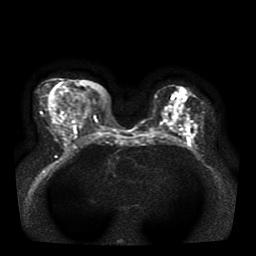
Breast MRI, one axial slice; position 18 of 39 along the scan axis; diffusion-weighted series; image 2 of 4 stored at this slice position (different b-values; order by instance number); 1.5 T; 5 mm slice thickness; 256 × 256 image matrix, field of view 330 × 330 mm. Female patient.
Annotated regions visible in this slice (outlined manually by an expert reader):
- tumour on diffusion-weighted imaging: box from (x=187, y=127) to (x=191, y=136) px